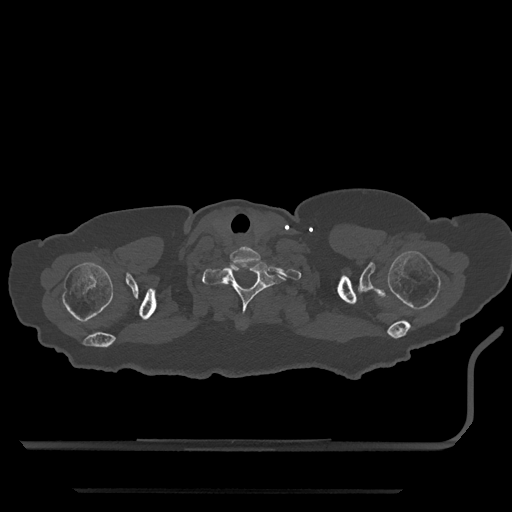
CT including the spine, one axial slice. Position 716 of 797 along the scan axis. Bone window (W 1800 / L 400 HU). 0.5 mm slice thickness. 512 × 512 image matrix, field of view 440 × 440 mm. Female patient, age 51 years. From the clinical record (not read from this slice): primary cancer: neuro; vertebrae with lytic lesions (as recorded): T8.
Structures marked on this image (semi-automatic segmentation, software-assisted and operator-edited):
- T1 vertebra: box from (x=202, y=261) to (x=286, y=314) px